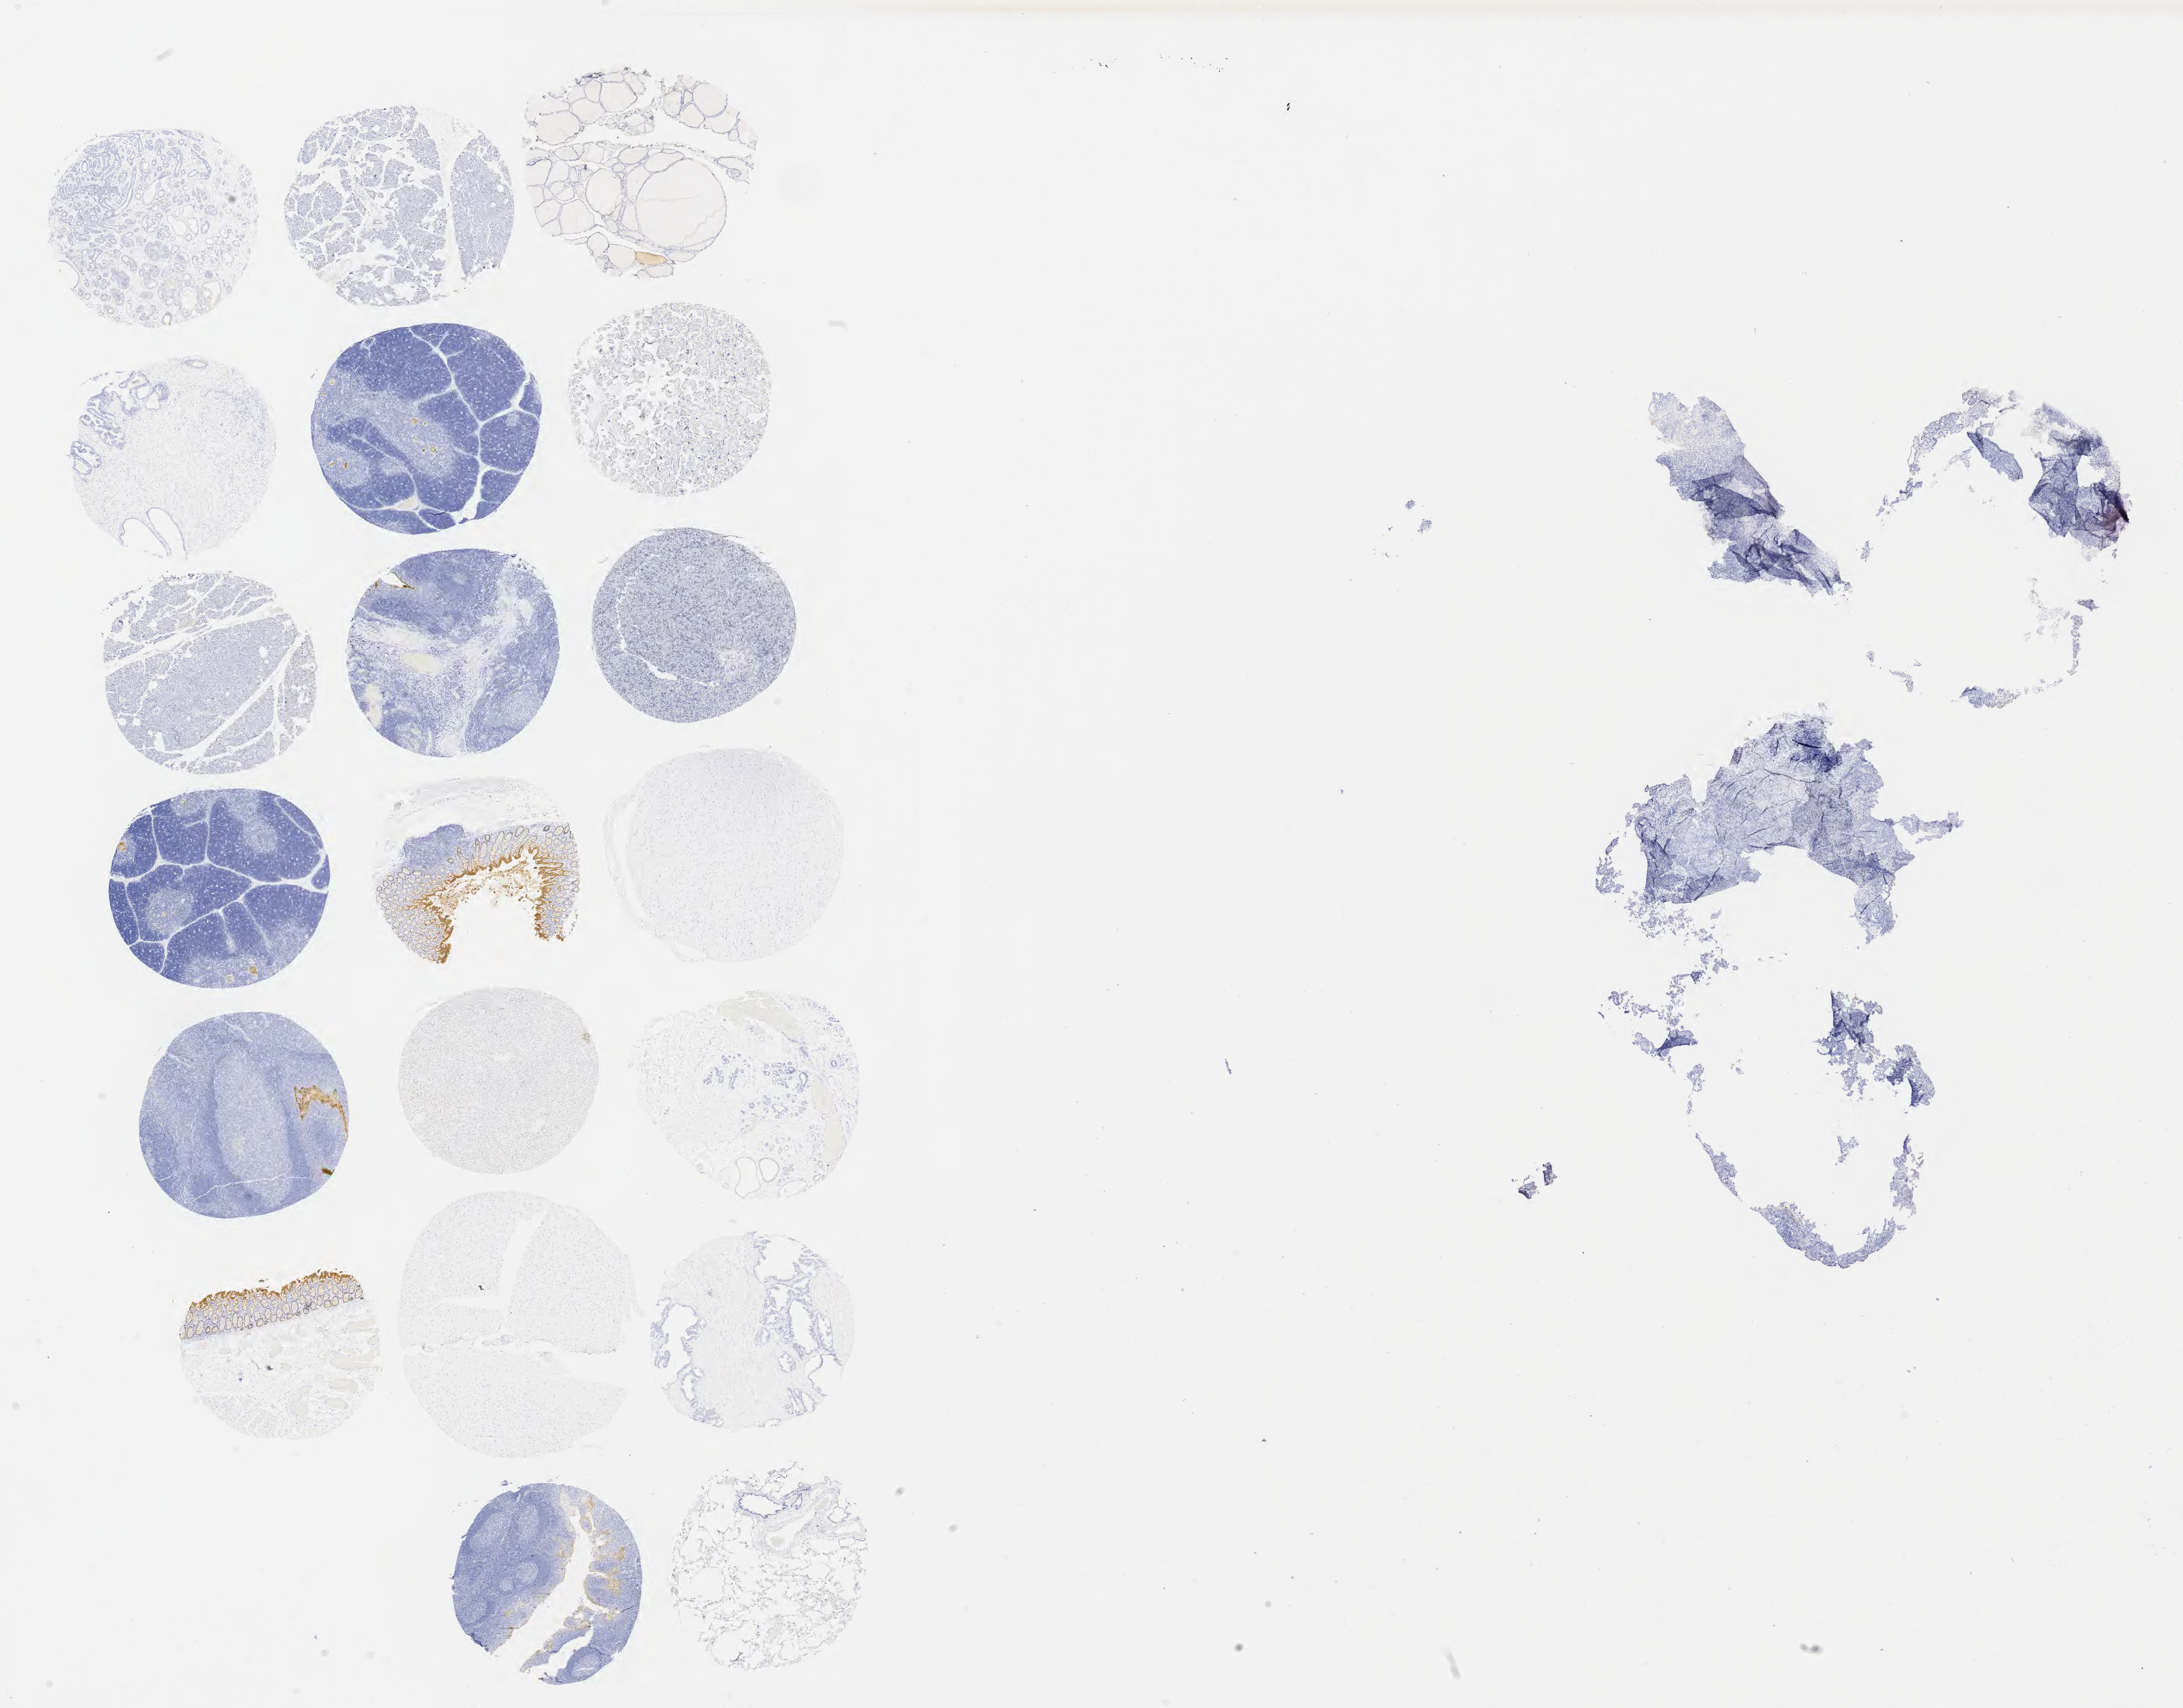
Whole-slide image, immunohistochemical stain for carcinoembryonic antigen (CEA), shown as a low-resolution overview of the whole scanned area (about 25.1 x 19.7 mm), specimen: tumor tissue, site: cervix. Patient: female, 48 years old.
Histologic diagnosis: Adenocarcinoma, NOS.